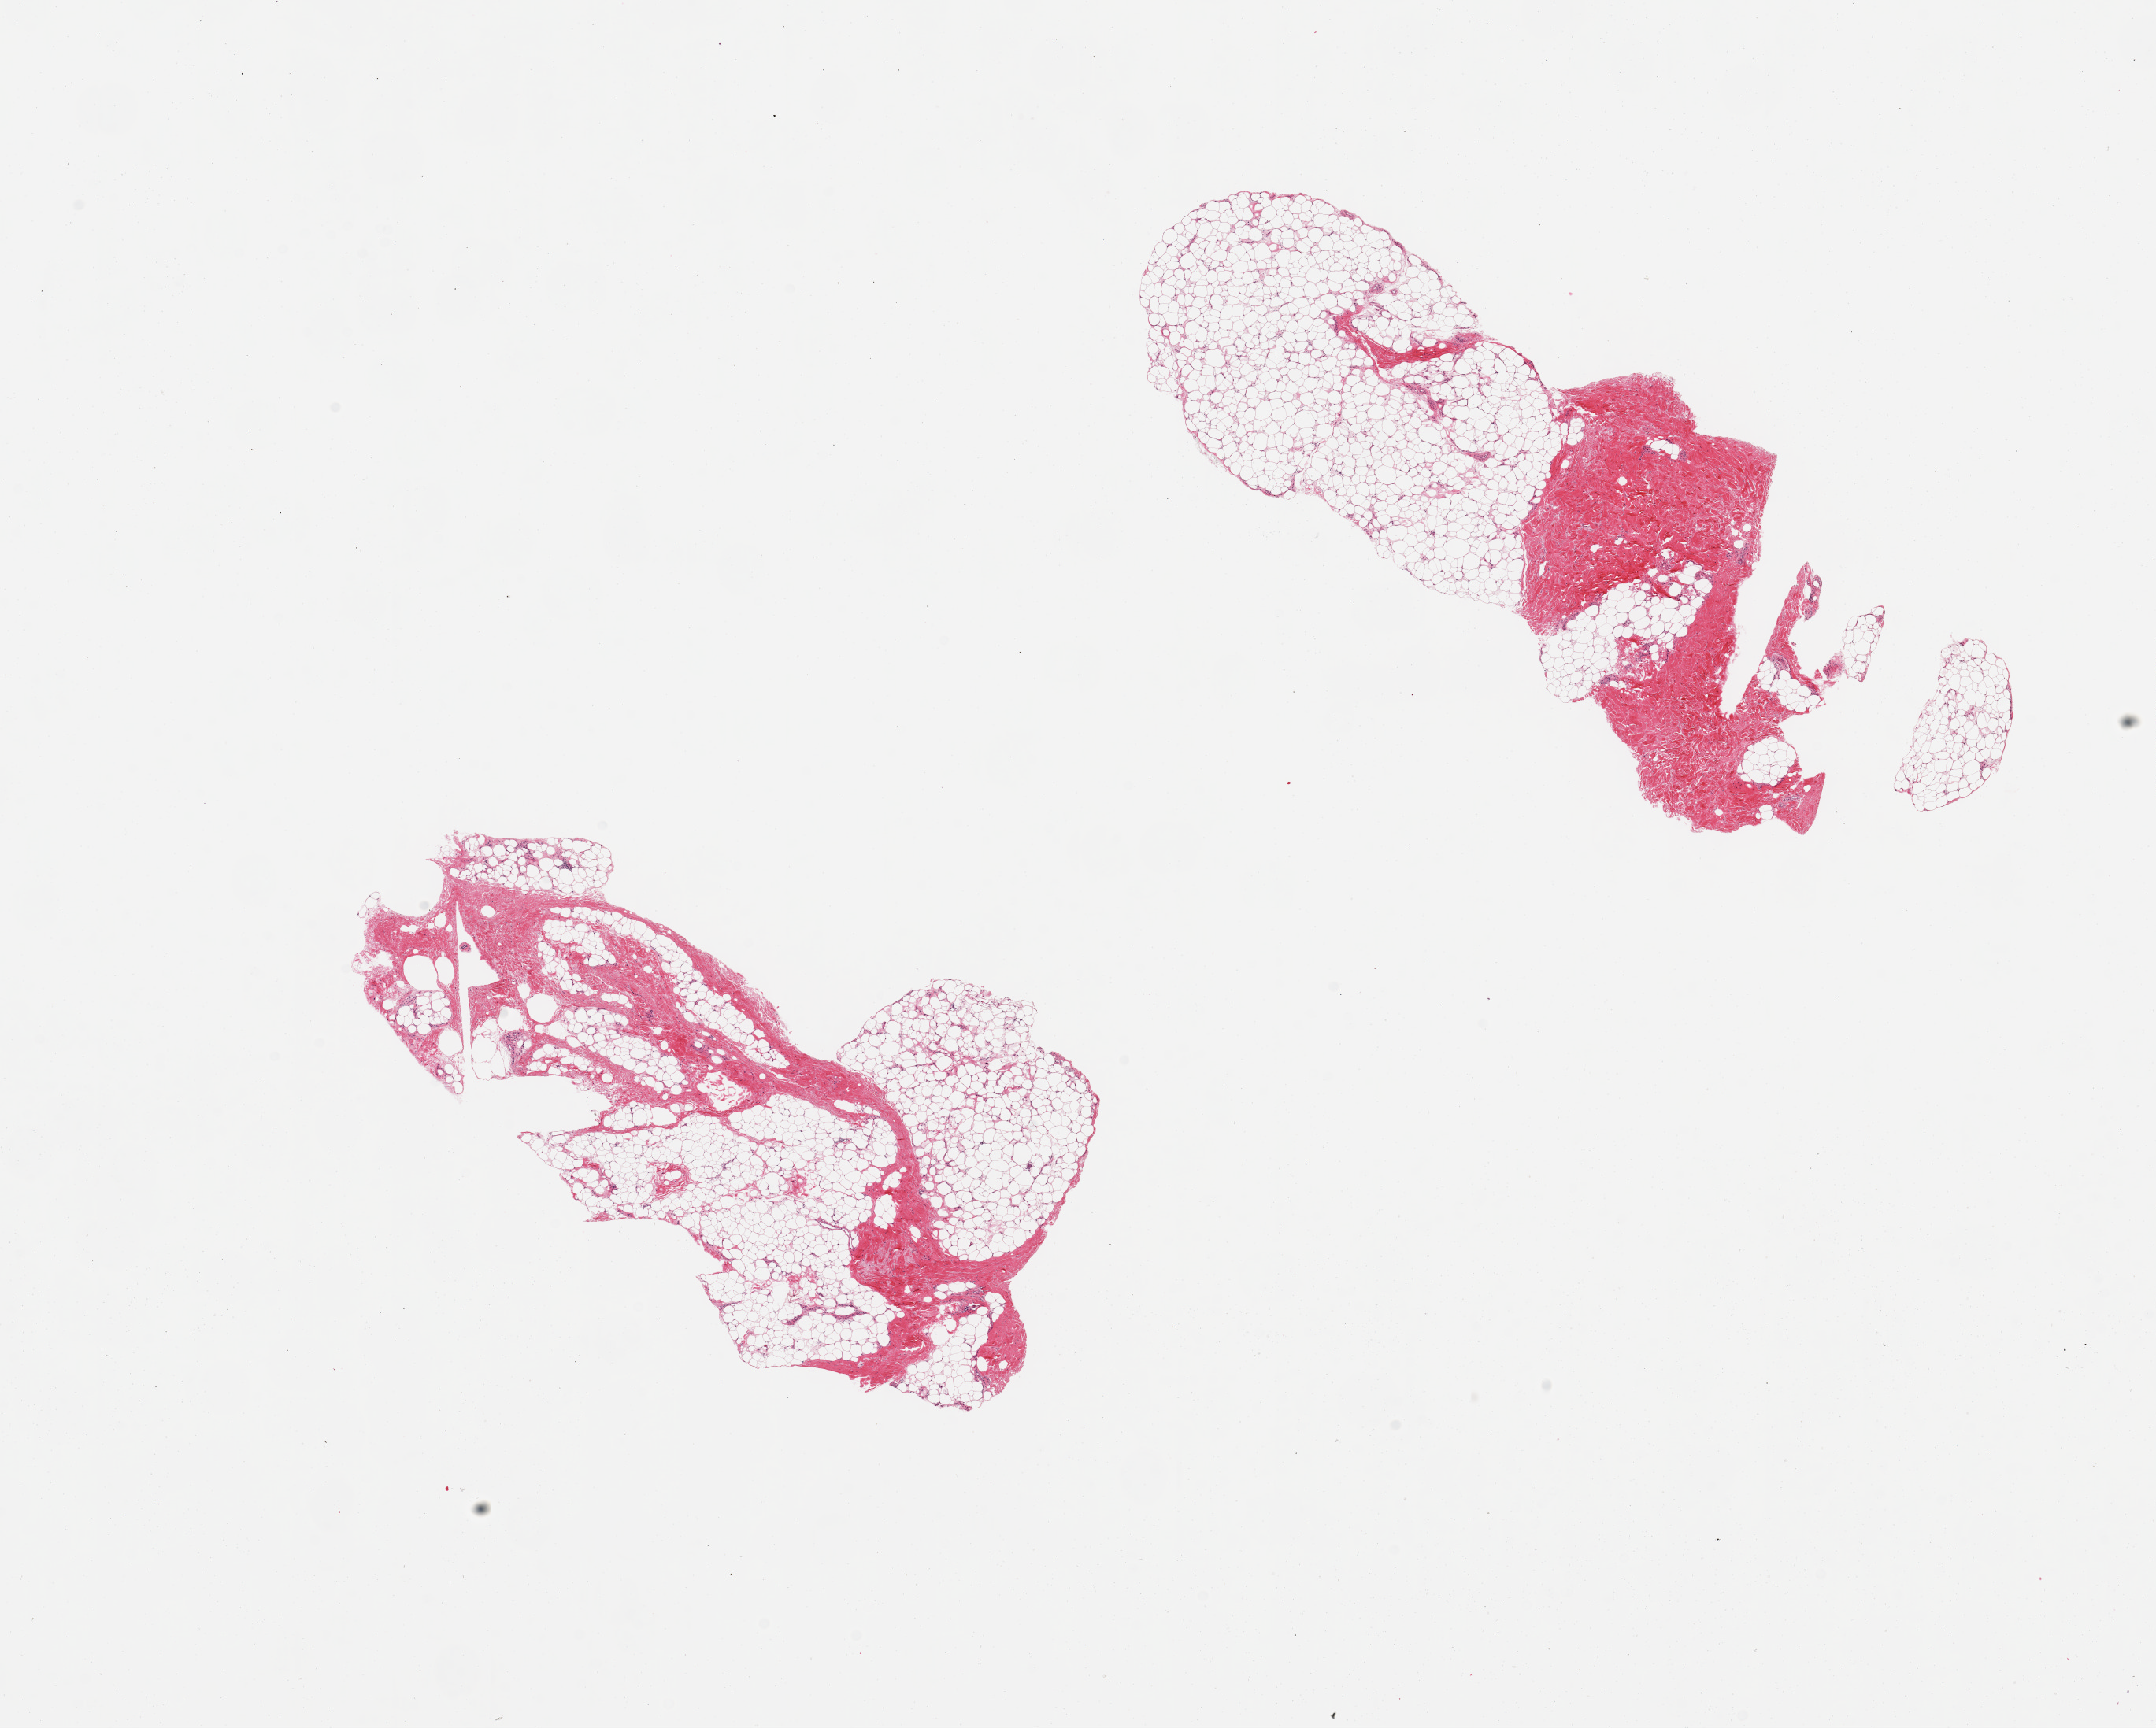
Digitized H&E-stained section — shown as a low-resolution overview of the whole scanned area (about 21.7 x 17.4 mm, from a 20x scan); PAXgene-fixed paraffin-embedded (PFPE) section; sampled site (target tissue): adipose tissue; donor tissue sample. Donor sex: female.
- review note (as recorded): 2 pieces, 20-30% fibrous